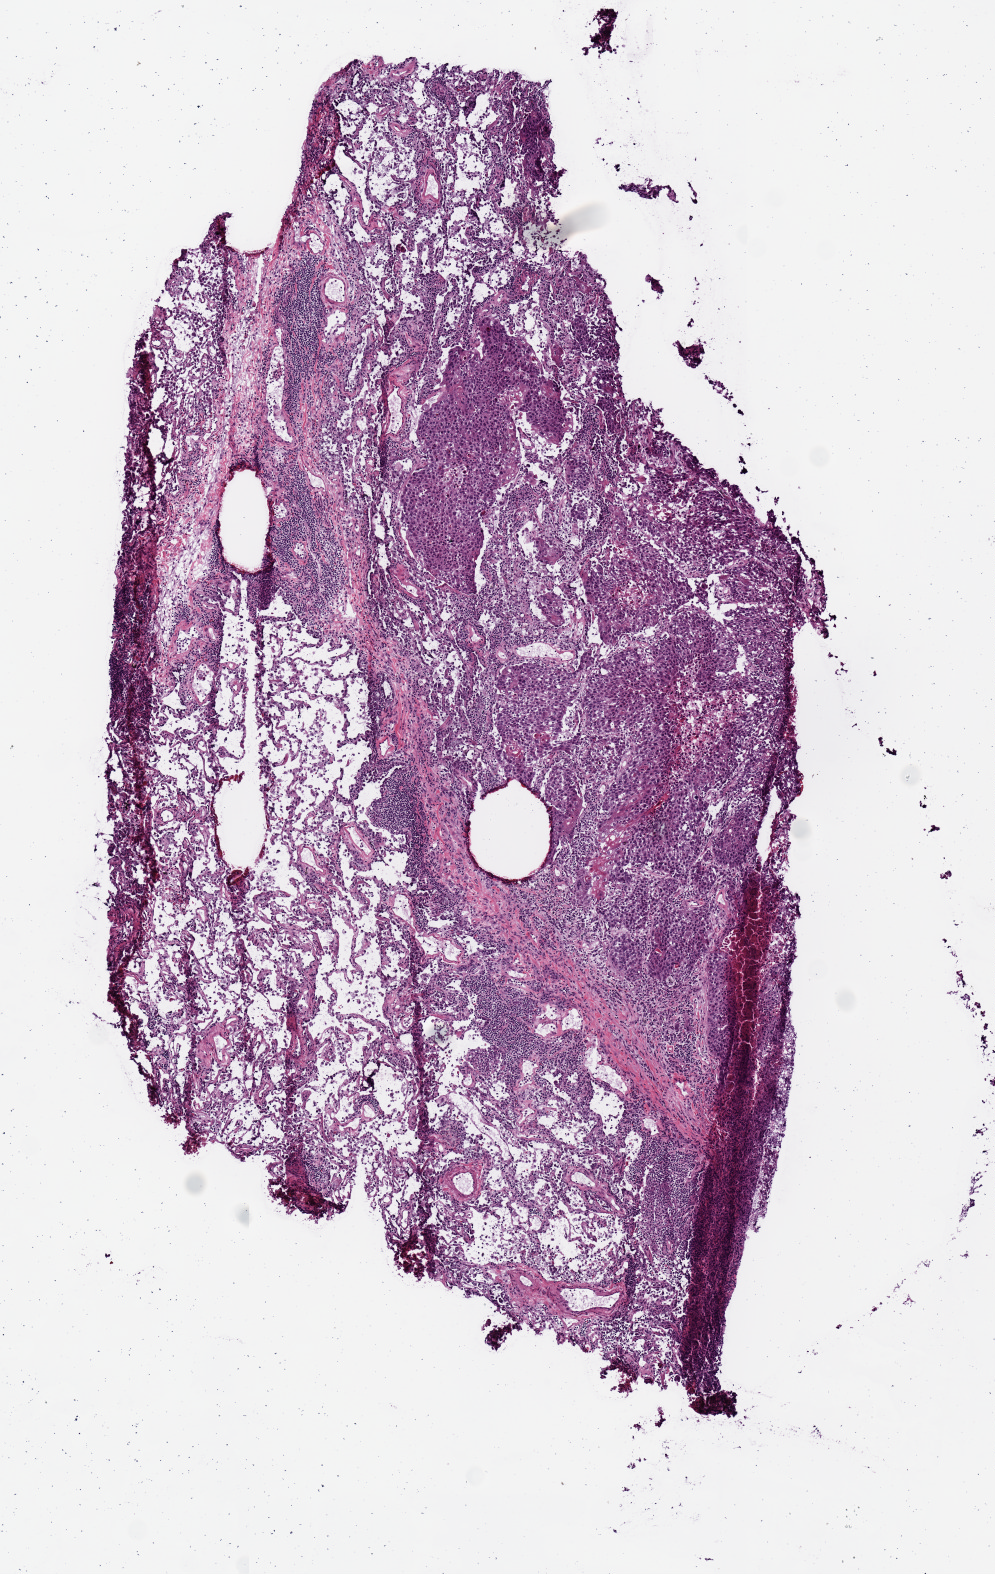
Whole-slide histology image, H&E, whole scanned area (about 3.9 x 6.2 mm) shown as a low-resolution overview, frozen section, lung, primary tumour sample. Male patient; age at initial diagnosis 76 years. Pathologist review of this section (percent, as recorded): tumour cells 80%, tumour nuclei 65%, normal cells 0%, stromal cells 15%, necrosis 5%.
Laterality: left. Diagnosis: Squamous cell carcinoma, NOS (upper lobe, lung). AJCC pathologic stage: IIIA (6th edition).